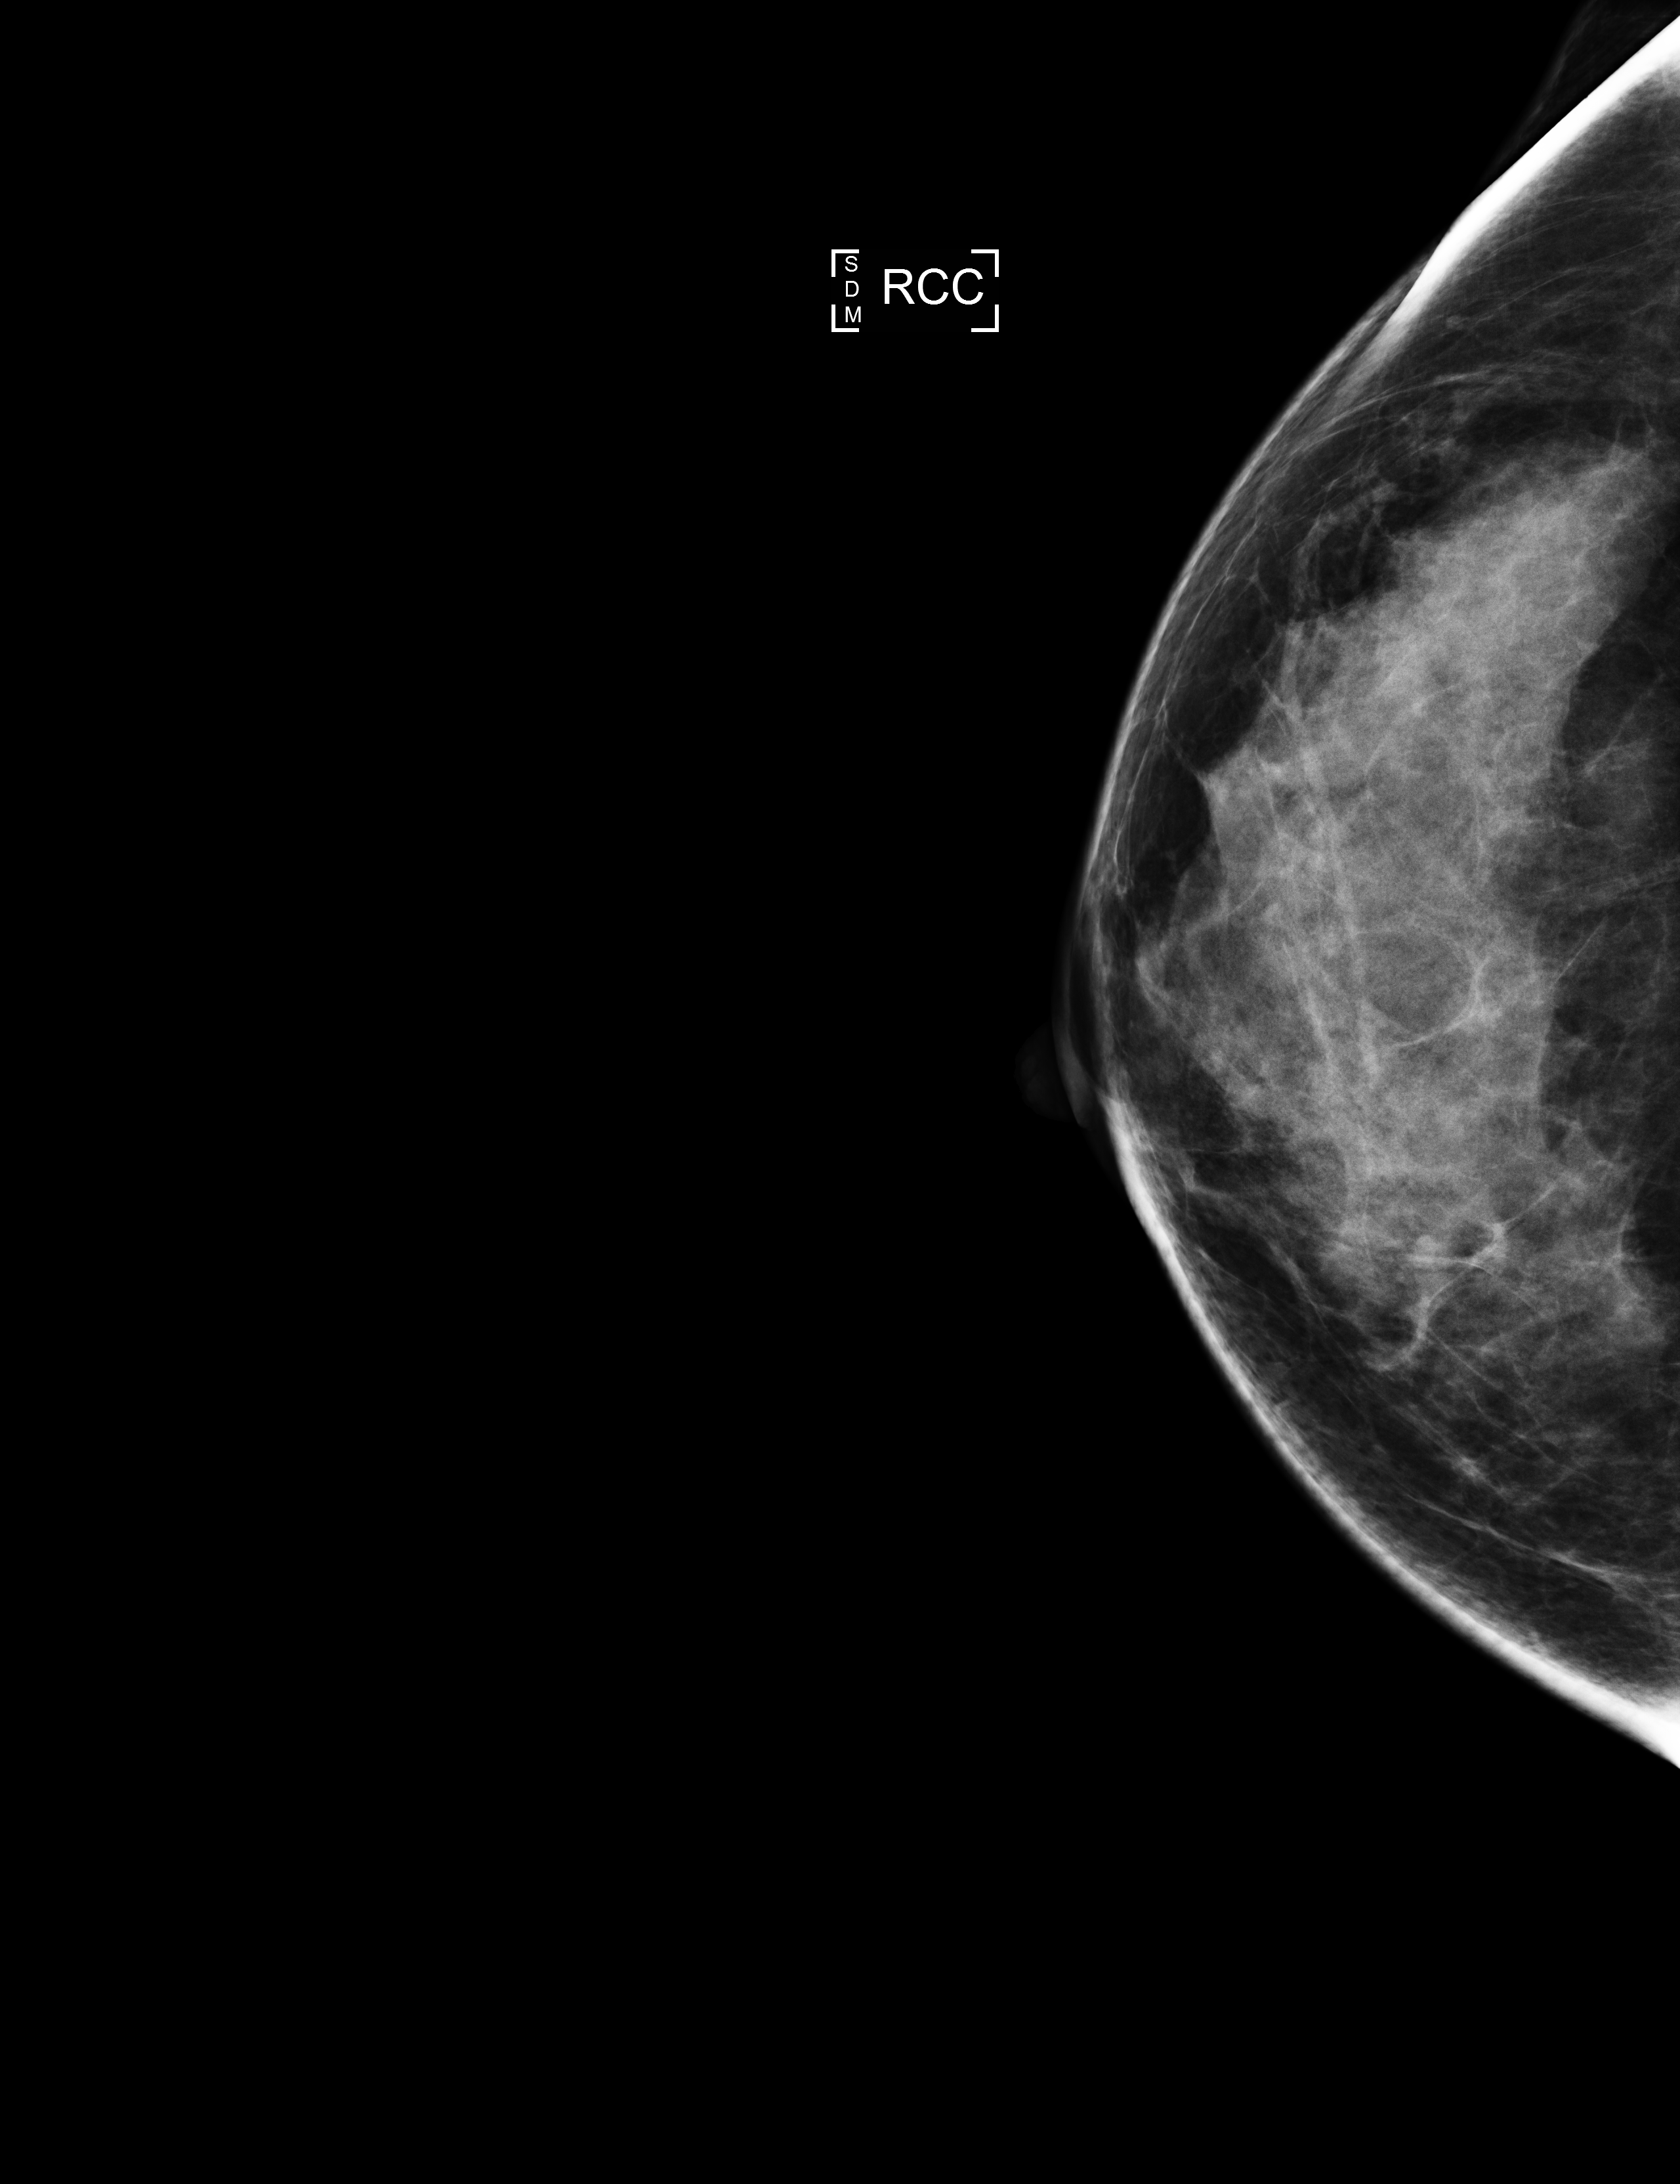
Screening examination, compressed breast thickness 63 mm, system: Selenia Dimensions. Patient aged 43 years (female).
Image type: full-field digital mammogram. Breast: right. Projection: CC view.